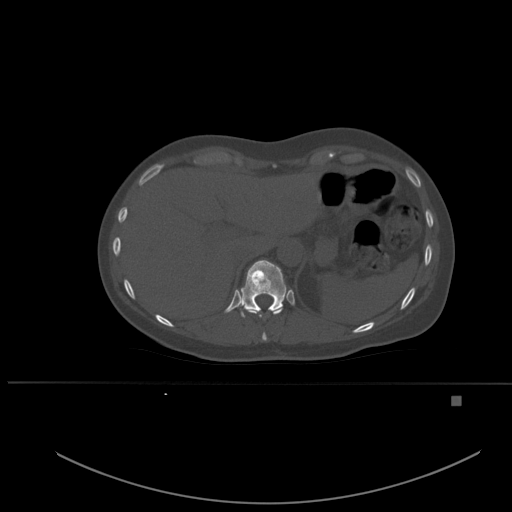
CT including the spine, one axial slice; slice 278 of 651 in the series (ordered by position); bone window (W 1800 / L 400 HU); 1.5 mm slice thickness; 512 × 512 image matrix, field of view 443 × 443 mm. Female patient, age 49 years. Case-level facts recorded for this patient, not image findings: primary cancer: breast; vertebrae with lytic lesions (as recorded): L3, T12, L4.
Outlined on this slice (semi-automatic segmentation, software-assisted and operator-edited):
- T10 vertebra: box from (x=247, y=307) to (x=283, y=341) px
- T11 vertebra: (x=238, y=260)–(x=287, y=318)